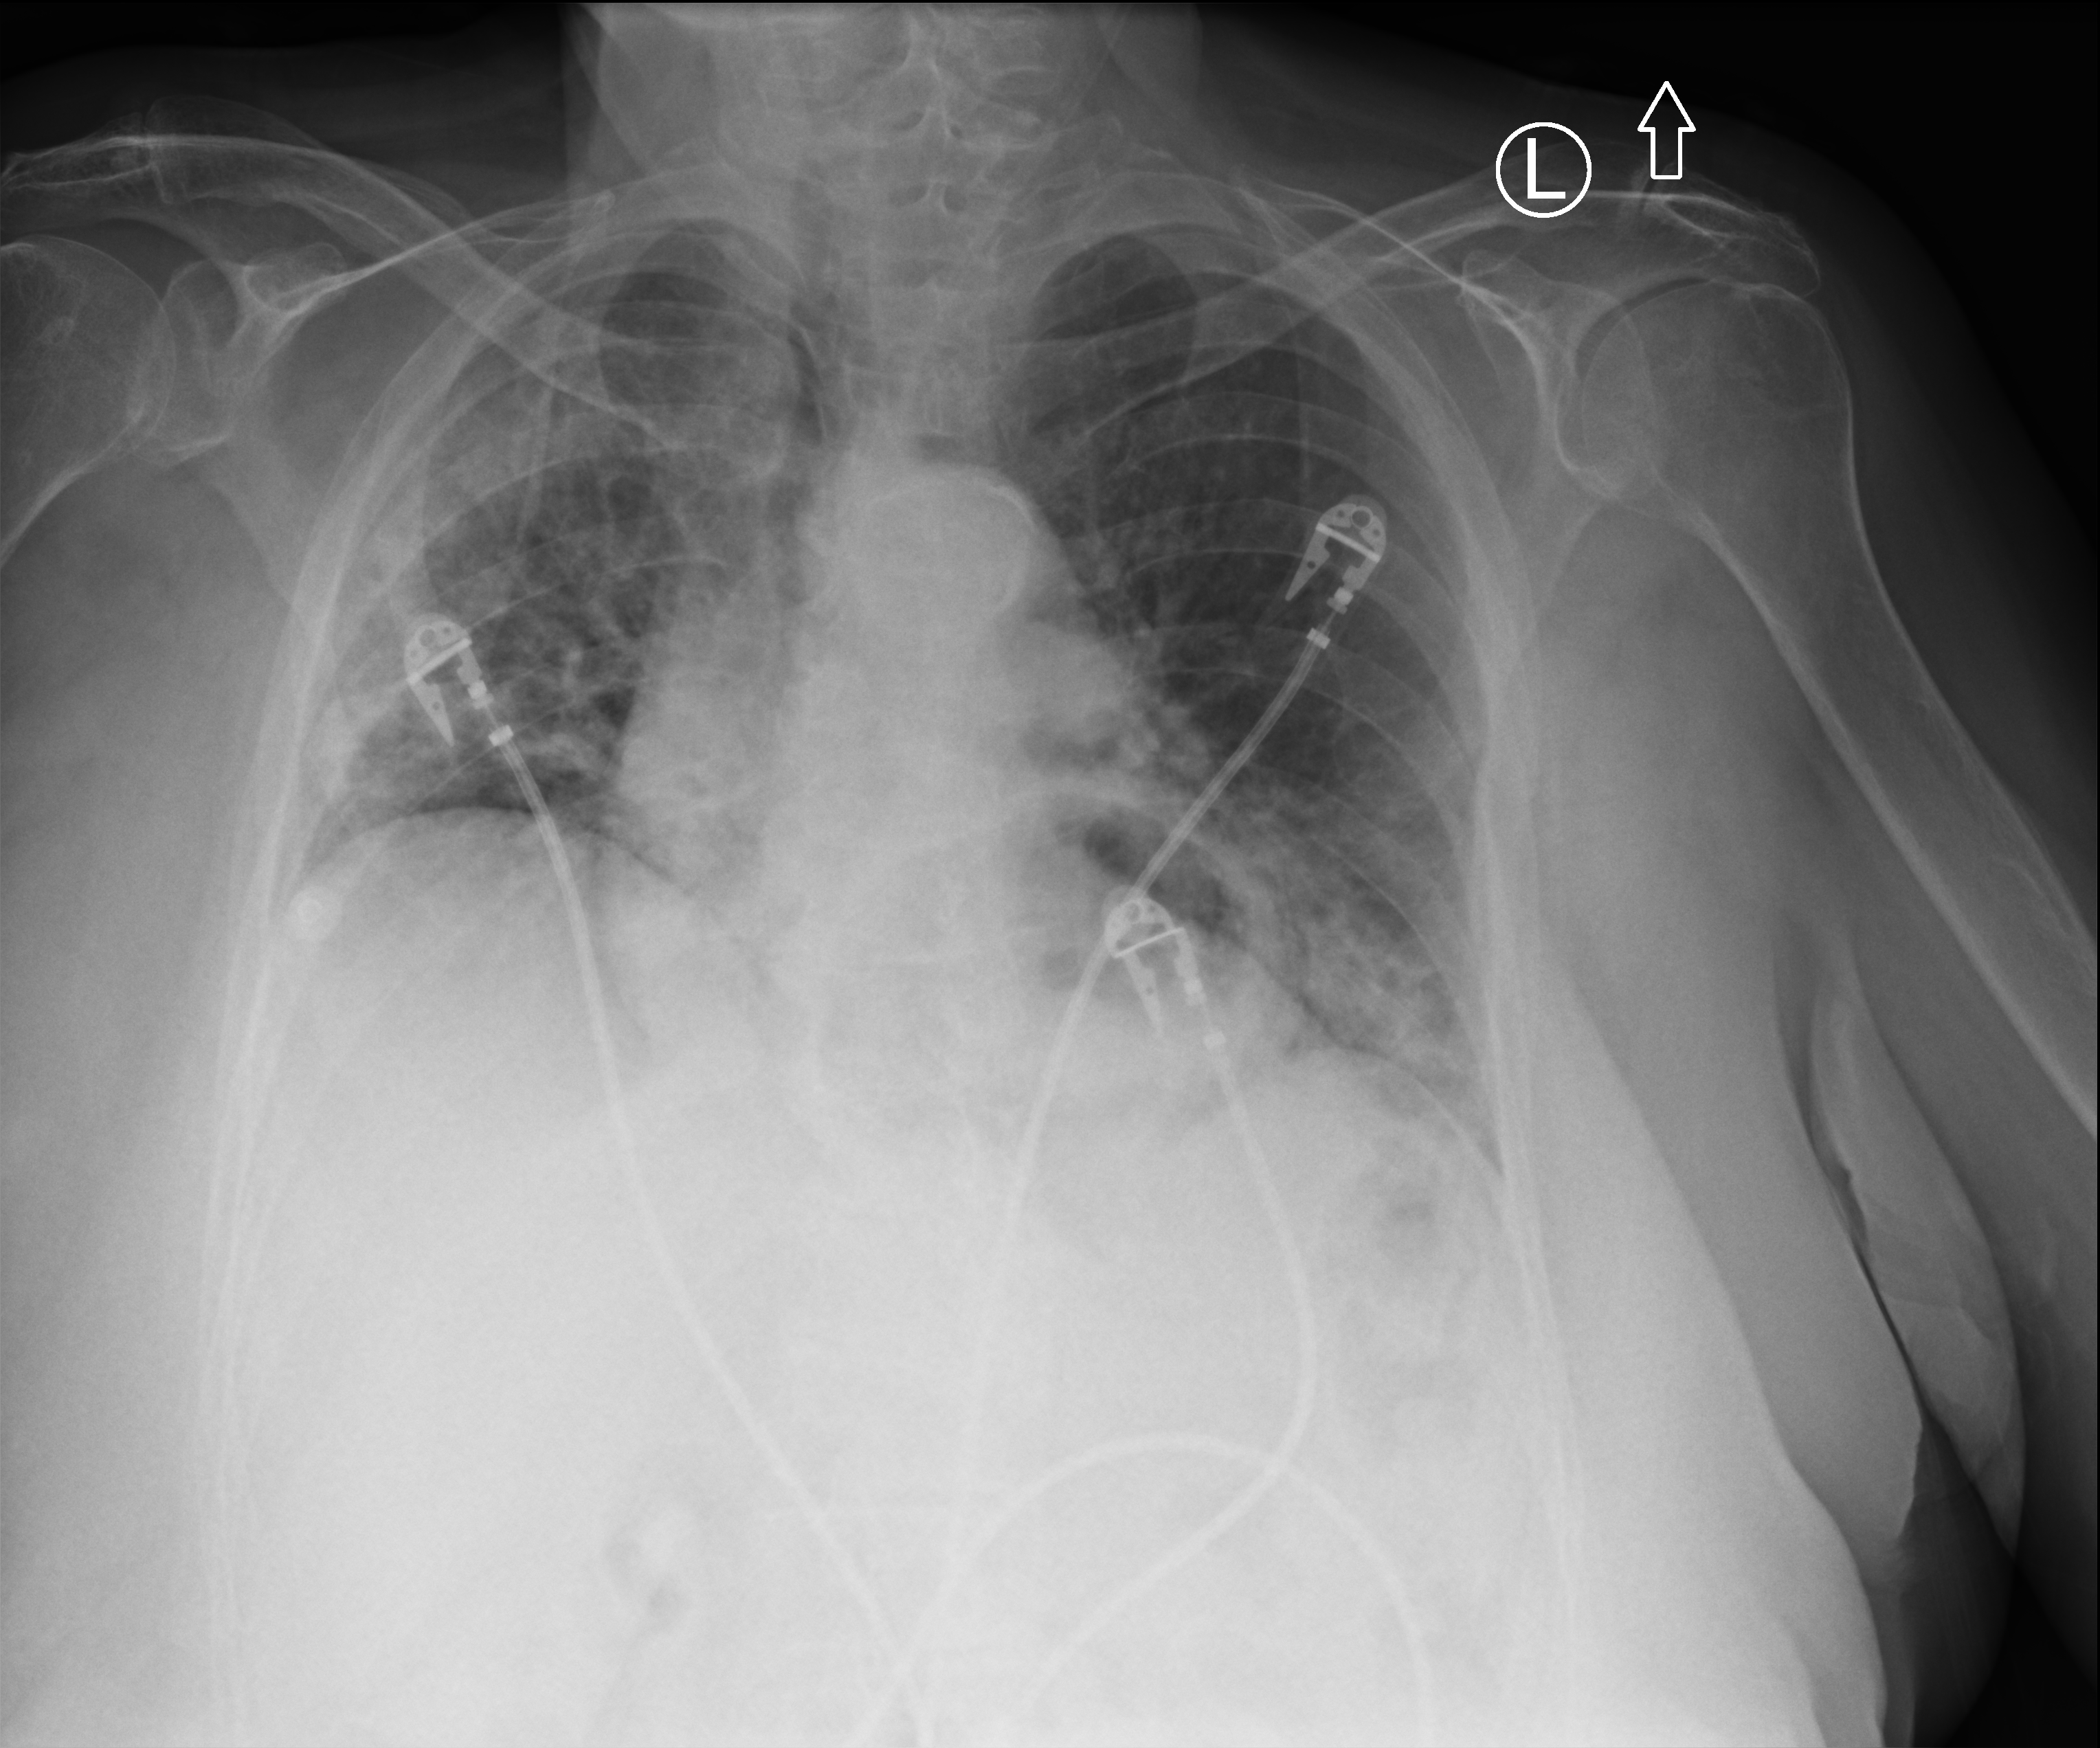
Portable chest radiograph; anteroposterior (AP) projection. Patient hospitalised with COVID-19; female, aged 75–90 years.
From the hospital-stay record, not from the radiograph (when in the stay this image was taken is not recorded): admitted to intensive care during this hospital stay: no; length of hospital stay: 12 days.